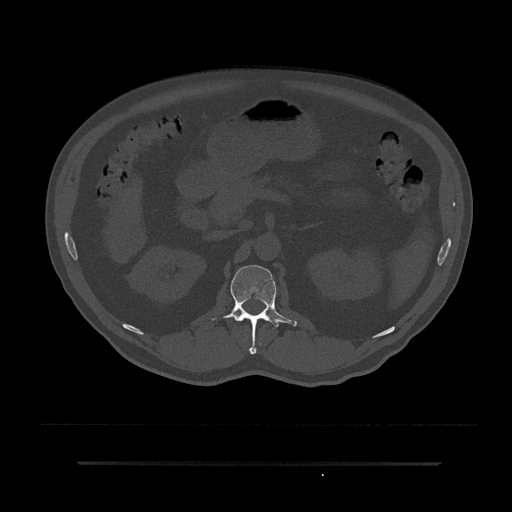
CT including the spine, one axial slice. Slice 147 of 797 in the series (ordered by position). Reconstruction kernel Br40s/3. 120 kVp. Bone window (W 1800 / L 400 HU). 0.5 mm slice thickness. 512 × 512 image matrix, field of view 464 × 464 mm. Patient: male, 59 years. From the clinical record (not read from this slice): primary cancer: bile ducts; vertebrae with lytic lesions (as recorded): T10.
Annotated regions visible in this slice (semi-automatic segmentation, software-assisted and operator-edited):
- L1 vertebra: bounding box <211,265,297,354> (left, top, right, bottom; pixels)